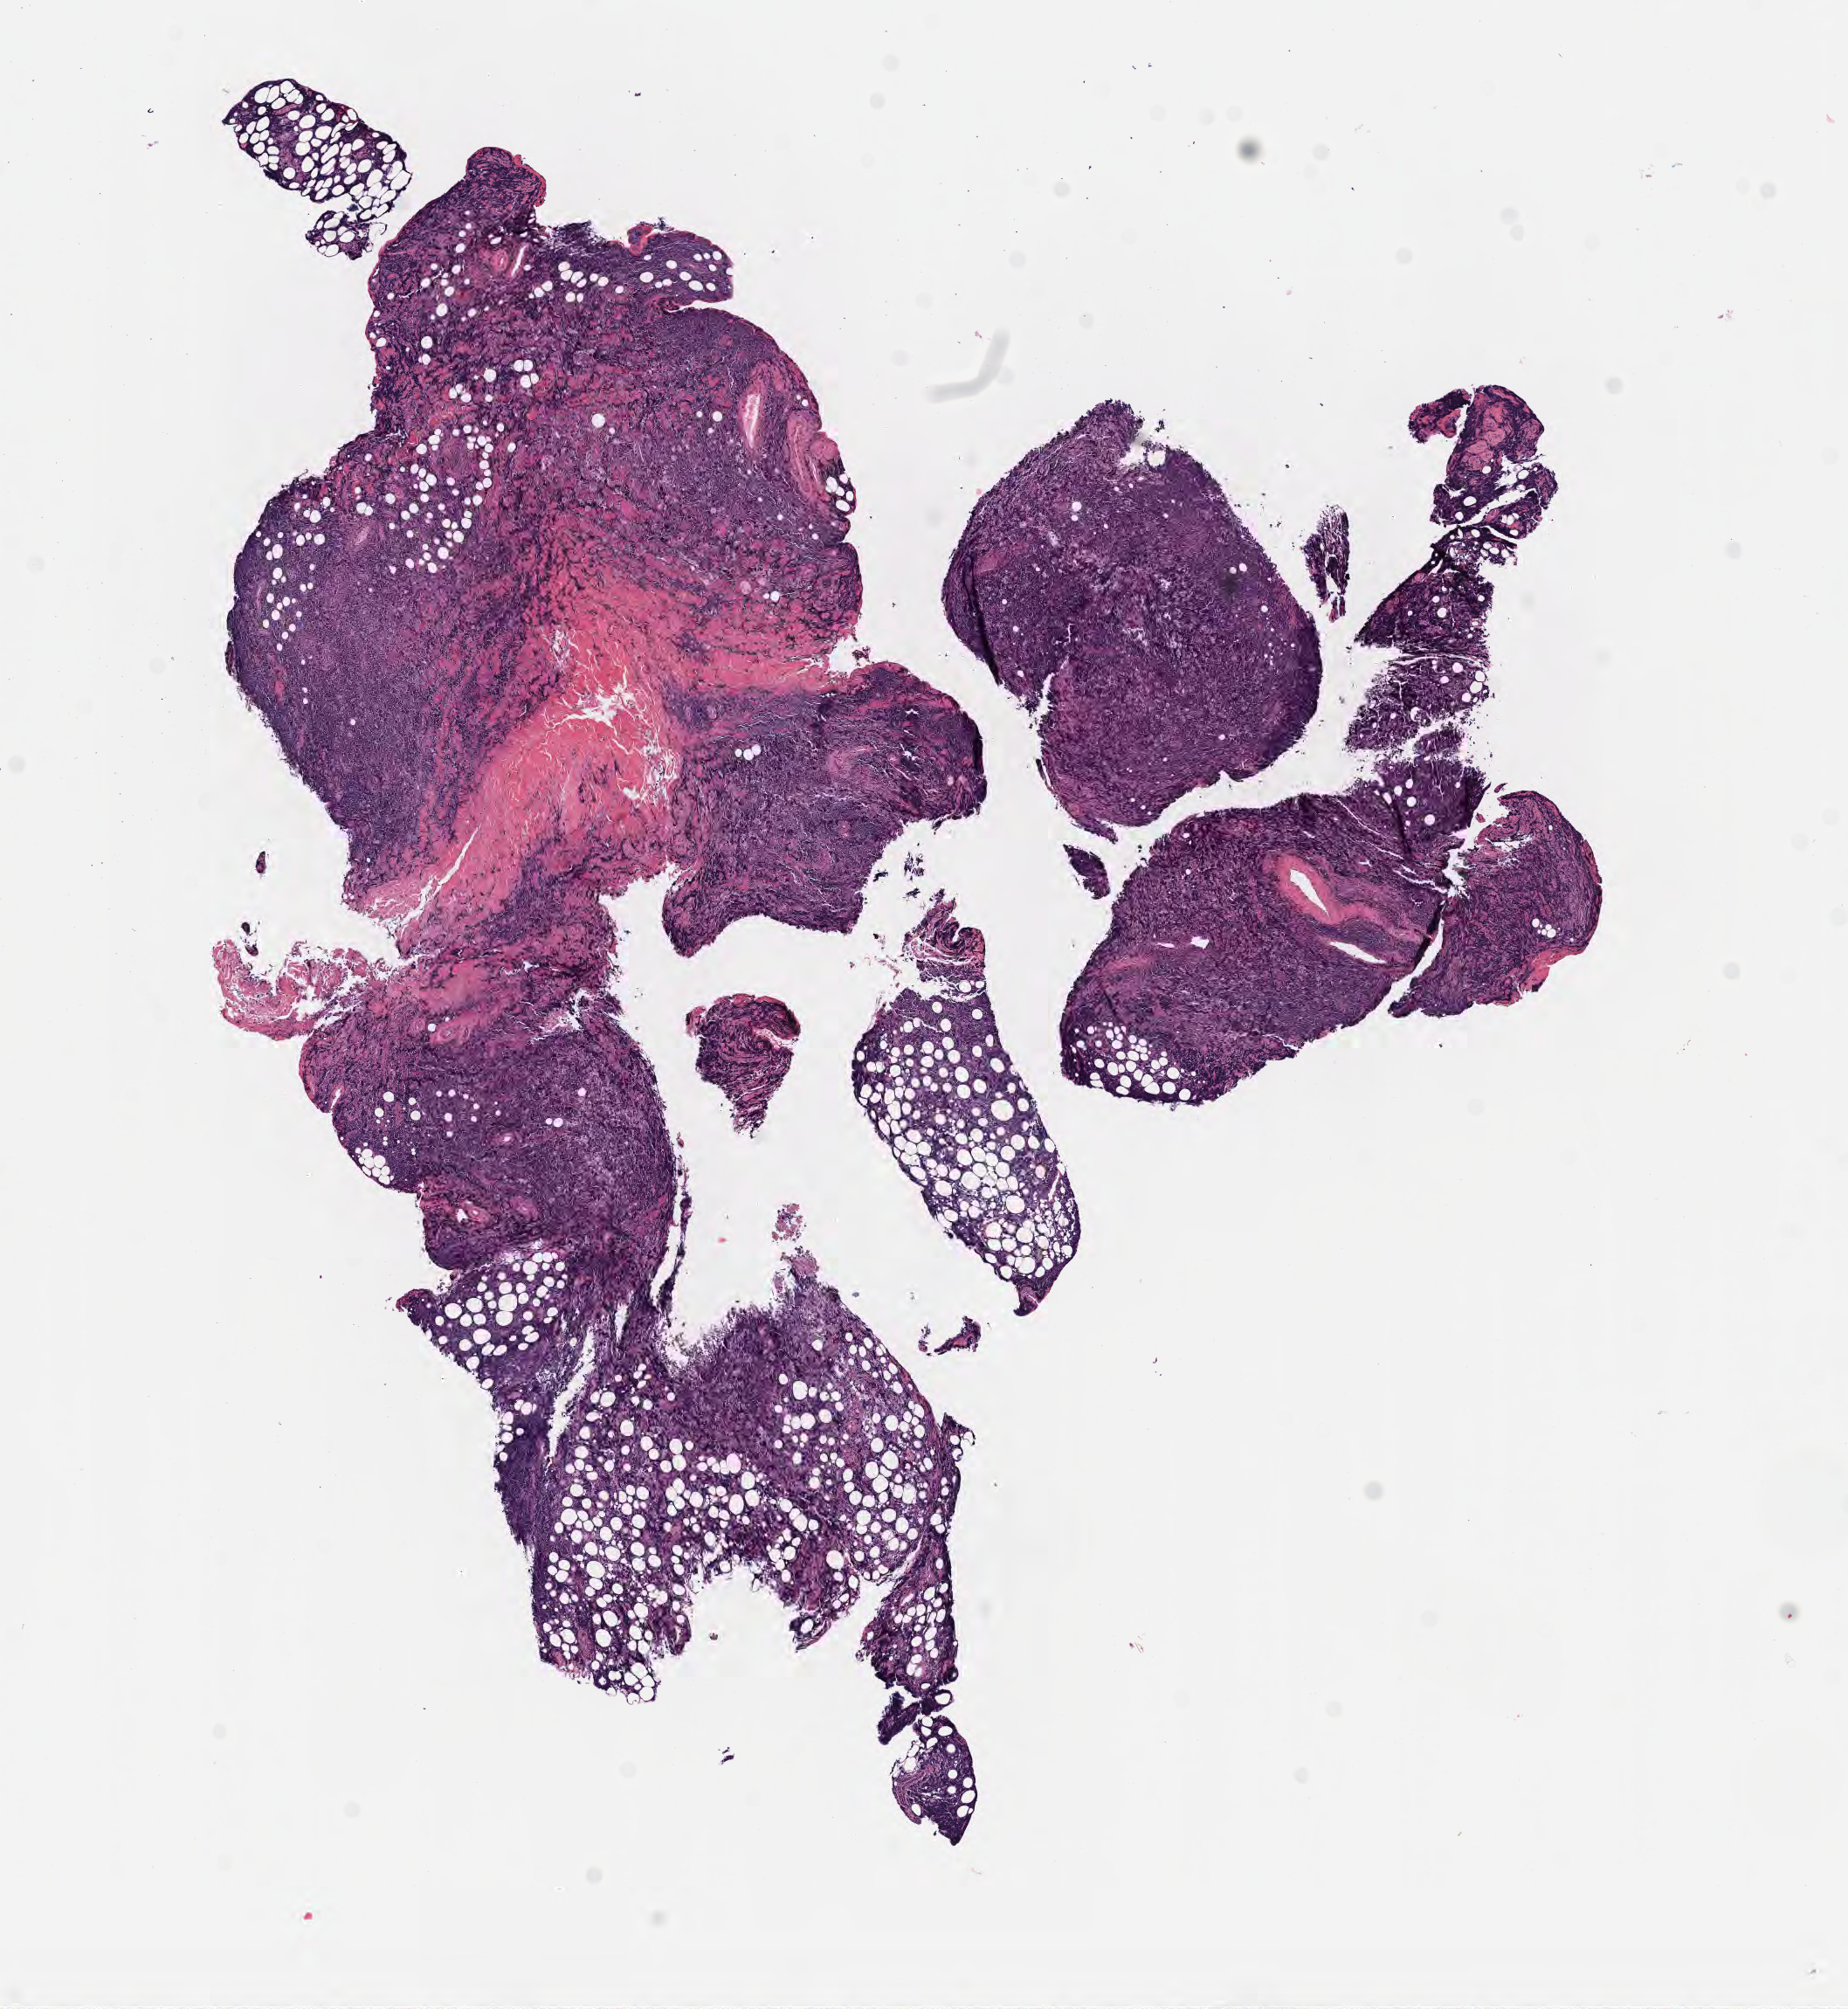
Digitized hematoxylin and eosin (H&E)-stained section, whole scanned area (about 8.6 x 9.3 mm) shown as a low-resolution overview, tumor tissue, anatomic site: orbit. Patient male; 20 years old.
Diagnosis: Burkitt lymphoma, NOS.